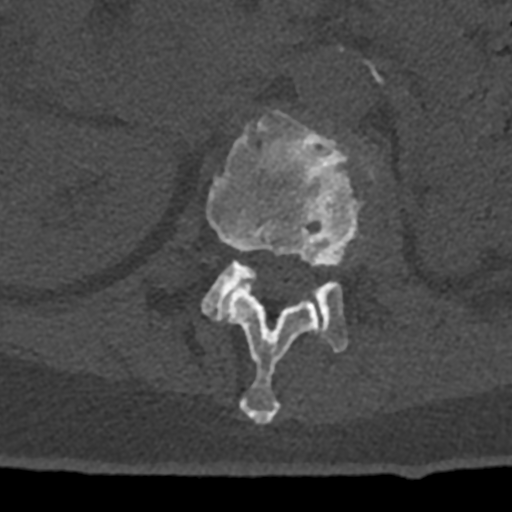
CT including the spine, one axial slice; slice 412 of 797 in the series (ordered by position); reconstruction kernel Br40s/3; 120 kVp; bone window (W 1800 / L 400 HU); 0.5 mm slice thickness; 512 × 512 image matrix, field of view 160 × 160 mm. Patient: male, 74 years. From the clinical record (not read from this slice): primary cancer: renal; vertebrae with lytic lesions (as recorded): T10, L1, L2, L3, L4, L5.
Outlined on this slice (semi-automatic segmentation, software-assisted and operator-edited):
- L1 vertebra: box from (x=206, y=110) to (x=363, y=424) px
- L2 vertebra: (x=202, y=261)–(x=348, y=353)